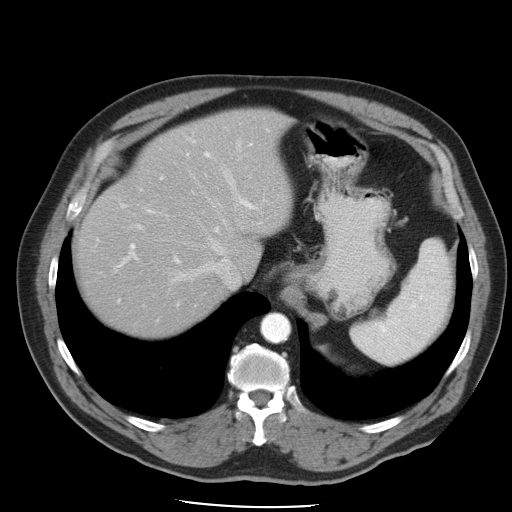
Contrast-enhanced abdominal CT, one axial slice. Position 38 of 49 along the scan axis. Intravenous contrast given. Soft-tissue window (W 400 / L 40 HU). 512 × 512 image matrix, field of view 395 × 395 mm. Male patient, age 68 years. From the clinical record (not read from this slice): diagnosis: colorectal cancer liver metastases, imaged before liver resection.
Annotated regions visible in this slice (outlined manually by an expert reader):
- hepatic veins: bounding box <170,193,244,287> (left, top, right, bottom; pixels)
- liver: <76,109,293,338>
- planned liver remnant (the part of the liver to remain after resection): <76,109,293,337>
- portal vein (with intrahepatic branches): <98,129,268,306>